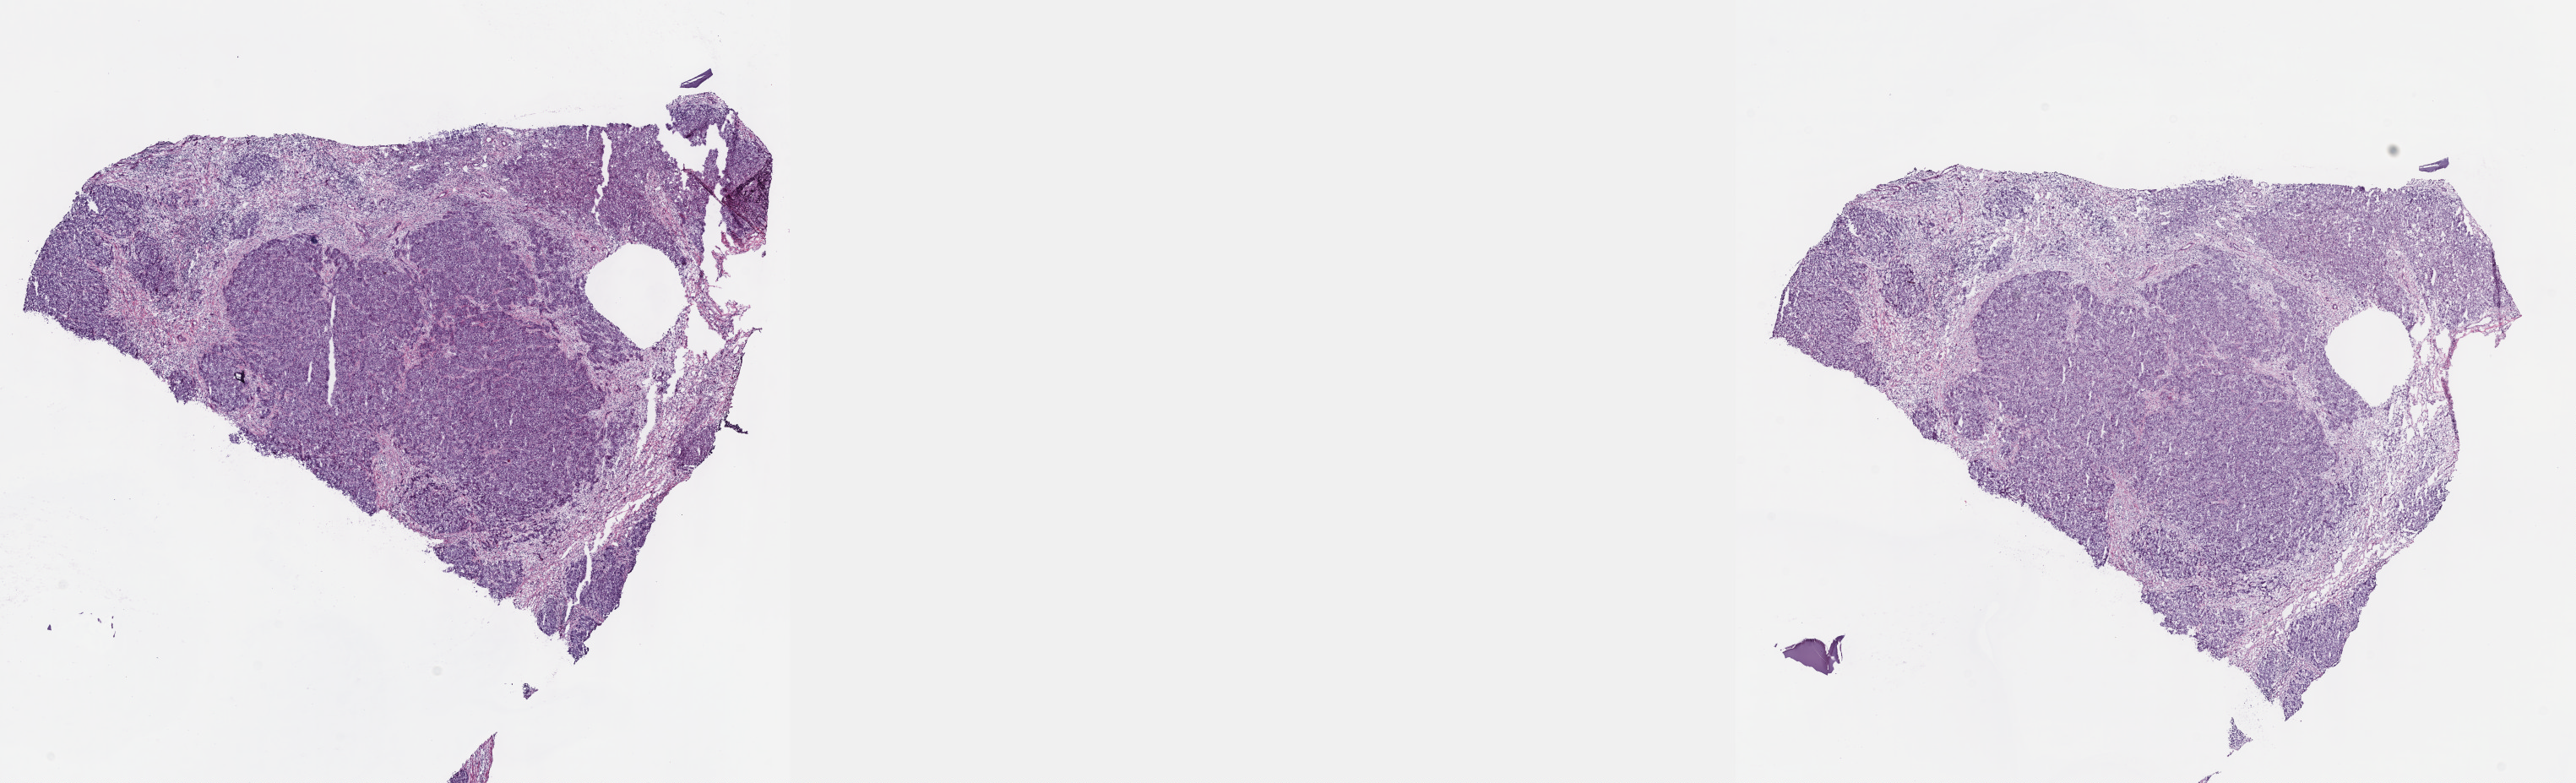
Whole-slide histology image, Hematoxylin and eosin (H&E) stained, shown as a low-resolution overview of the whole scanned area (about 24.6 x 7.5 mm, slide scanned at 40x); frozen section from the top of the tissue portion; liver, primary tumour sample. Male, age 68 years at initial diagnosis. Histologic grade: G2 (moderately differentiated). Composition of this section per pathologist review: tumour cells 90%, tumour nuclei 65%, normal cells 0%, stromal cells 10%, necrosis 0%. Inflammatory infiltration, as recorded: lymphocyte infiltration 0%, monocyte infiltration 0%, neutrophil infiltration 0%.
- diagnosis: Hepatocellular carcinoma, NOS
- TNM: T1 NX MX
- AJCC pathologic stage: I